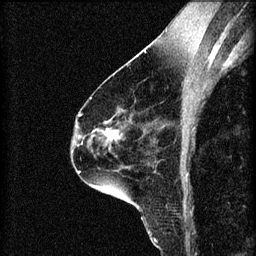
Breast MRI (dynamic contrast-enhanced), one sagittal slice. Position 39 of 60 along the scan axis. 3 images stored at this slice position (order not interpretable as contrast timing). 1.5 T. TE 4.2 ms, TR 8.2 ms. 256 × 256 image matrix, field of view 180 × 180 mm. Female patient, age 60 years.
Outlined on this slice (semi-automatically segmented with operator editing):
- analysis volume of interest (the breast-tissue region the enhancement analysis was run in; not a lesion): bounding box <89,116,124,151> (left, top, right, bottom; pixels)
- tumour enhancement mask (voxels above the 70 % enhancement threshold inside the analysis volume of interest): <104,122,119,141>